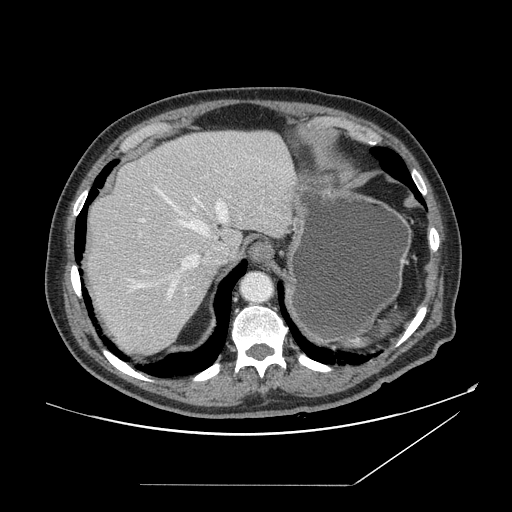
Contrast-enhanced abdominal CT, one axial slice. Position 124 of 166 along the scan axis. 120 kVp. Intravenous contrast given. Soft-tissue window (W 400 / L 40 HU). 512 × 512 image matrix, field of view 416 × 416 mm. Male patient, age 80 years. From the clinical record (not read from this slice): diagnosis: colorectal cancer liver metastases, imaged before liver resection; multiple liver metastases: no; largest metastasis: 2.2 cm; disease in both lobes: no.
Structures marked on this image (outlined manually by an expert reader):
- hepatic veins: bounding box [x1, y1, x2, y2] px = [131, 190, 242, 300]
- liver: [85, 131, 294, 355]
- planned liver remnant (the part of the liver to remain after resection): [87, 131, 294, 256]
- portal vein (with intrahepatic branches): [143, 208, 196, 273]